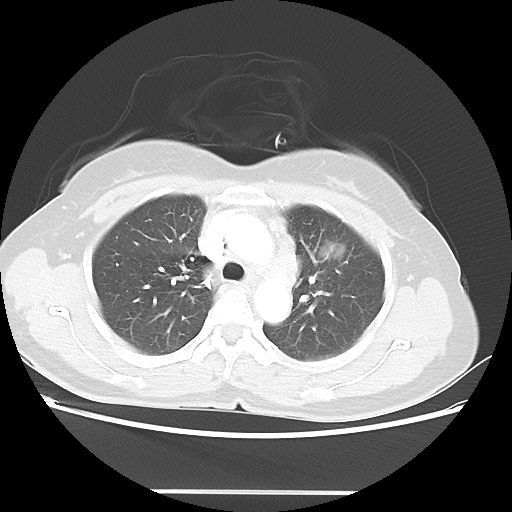
Chest CT, one axial slice. Slice 33 of 46 in the series (ordered by position). 100 kVp. Lung window (W 1500 / L -600 HU). 5 mm slice thickness. 512 × 512 image matrix, field of view 360 × 360 mm. Patient: female, 50 years. Case-level facts recorded for this patient, not image findings: clinical TNM (as recorded): T1c N1 M0; histopathological grade: G3.
Annotated regions visible in this slice (rectangle marked by the reading radiologist):
- lung tumour (recorded histology: adenocarcinoma): box from (x=319, y=239) to (x=348, y=262) px